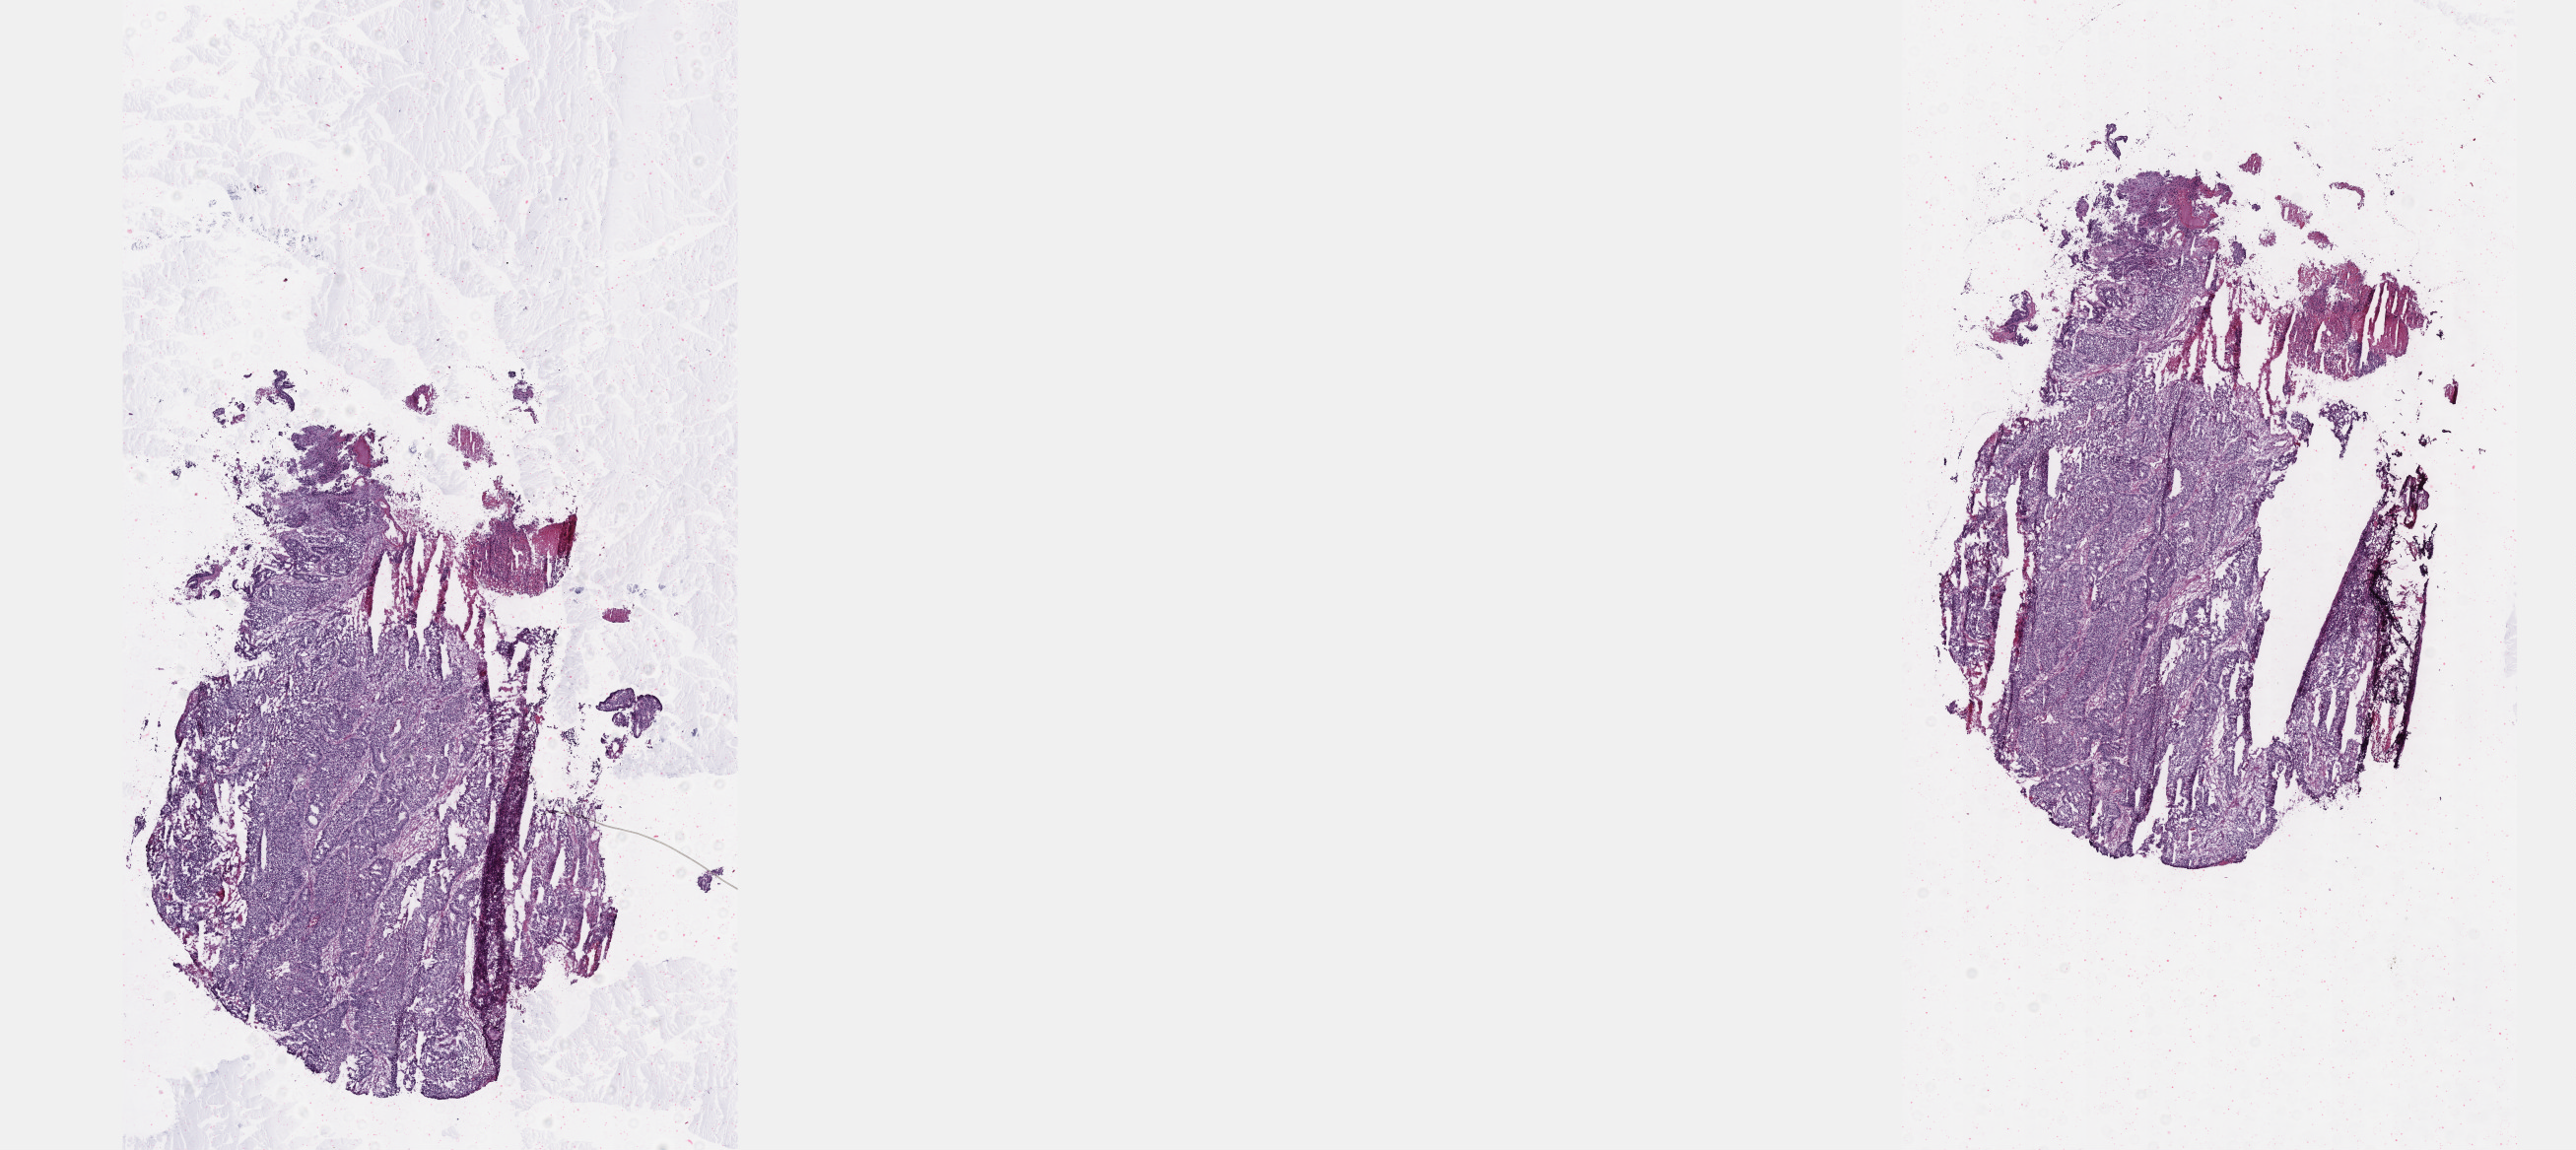
Hematoxylin and eosin (H&E) stained whole-slide image, low-resolution overview of the scanned area, about 21.1 x 9.4 mm (from a 40x scan); frozen section from the top of the tissue portion; primary tumour sample from the colon. Female patient; age at initial diagnosis 68 years. Composition of this section per pathologist review: tumour cells 90%, tumour nuclei 95%, normal cells 0%, stromal cells 5%, necrosis 5%. Infiltration values recorded for this section: lymphocyte infiltration 1%, monocyte infiltration 1%, neutrophil infiltration 1%.
Lymph nodes positive (case pathology): 1 of 12 examined. AJCC pathologic stage: IV (6th edition). Diagnosis: Carcinoma, NOS (sigmoid colon).